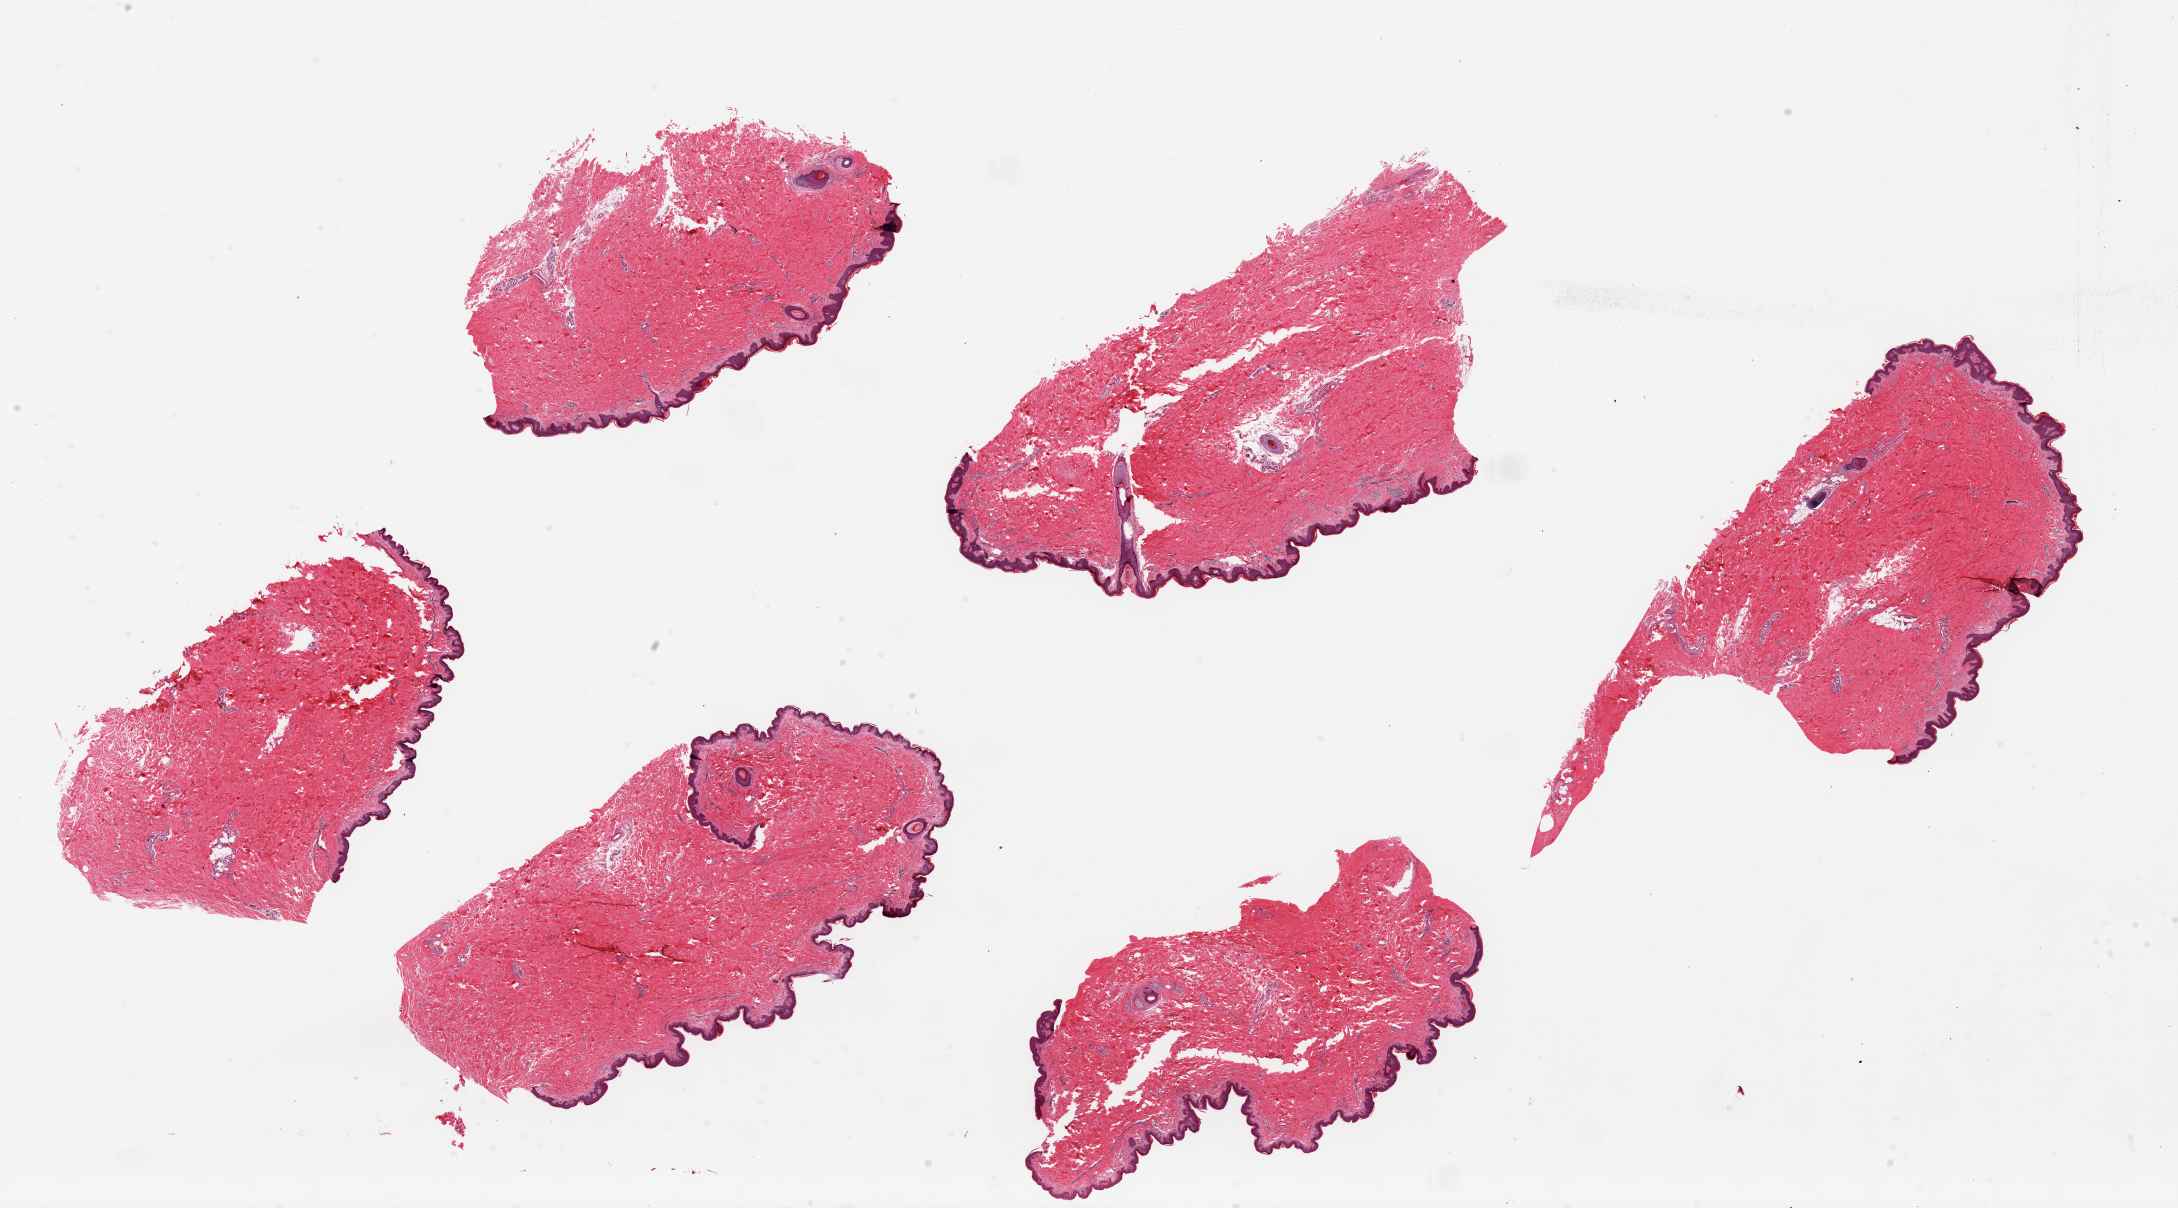
Digitized haematoxylin and eosin-stained section, brightfield, low-resolution overview of the scanned area, about 34.5 x 19.1 mm (slide scanned at 20x), PAXgene-fixed, paraffin-embedded tissue, target tissue: skin of suprapubic region, tissue donor sample. Donor: male.
Review note (as recorded): 6 pieces, up to 11x5mm; well trimmed of subcutaneous adipose.